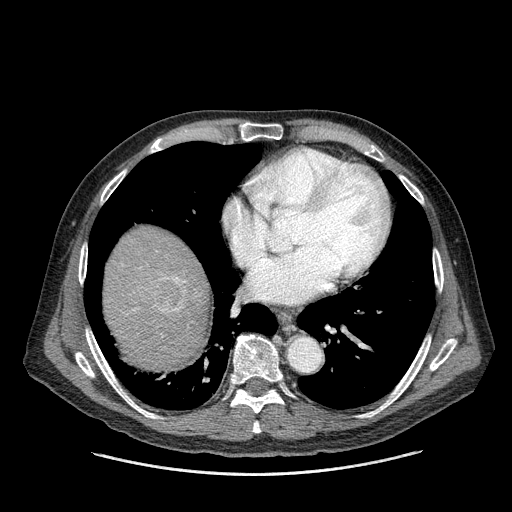
Contrast-enhanced abdominal CT (liver protocol), one axial slice; position 150 of 180 along the scan axis; reconstruction kernel STANDARD; 120 kVp; one of 2 acquisitions stored at this slice position; soft-tissue window (W 400 / L 40 HU); 2.5 mm slice thickness; 512 × 512 image matrix, field of view 420 × 420 mm. From the clinical record (not read from this slice): diagnosis: hepatocellular carcinoma (patient treated with transarterial chemoembolisation; whether this scan precedes or follows treatment is not stated here); TNM stage (as recorded): Stage-II; Child-Pugh class: A.
Structures marked on this image (semi-automatically segmented with operator editing):
- liver parenchyma outside the tumour (the mass and vessels are separate outlines, so this box may not span the whole liver): bounding box [x1, y1, x2, y2] px = [104, 226, 210, 368]
- mass: [146, 276, 189, 315]